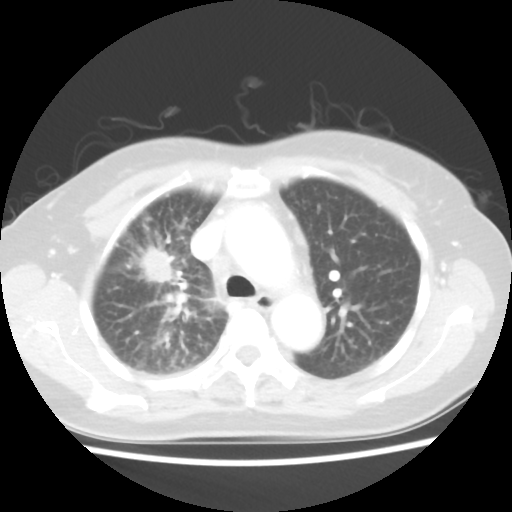
Chest CT, one axial slice. Position 32 of 48 along the scan axis. 100 kVp. Lung window (W 1500 / L -600 HU). 5 mm slice thickness. 512 × 512 image matrix, field of view 312 × 312 mm. Female patient, age 55 years. From the clinical record (not read from this slice): clinical TNM (as recorded): T1b N3 M1a.
Structures marked on this image (bounding box drawn by a radiologist):
- lung tumour (recorded histology: adenocarcinoma): bounding box [x1, y1, x2, y2] px = [142, 247, 175, 282]